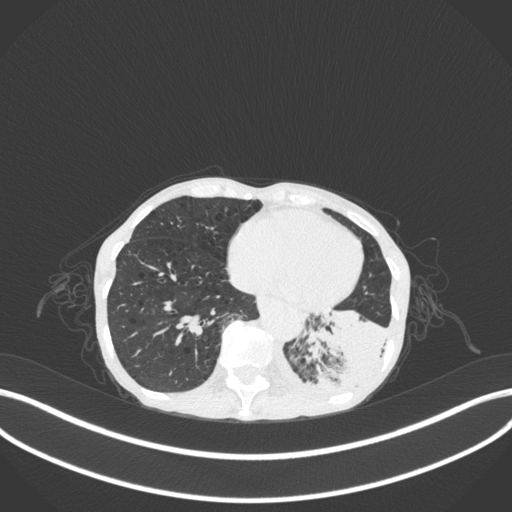
Chest CT, one axial slice; slice 64 of 347 in the series (ordered by position); reconstruction kernel B31f; 120 kVp; lung window (W 1500 / L -600 HU); 1 mm slice thickness; 512 × 512 image matrix, field of view 400 × 400 mm. Patient: female, 70 years. From the clinical record (not read from this slice): clinical TNM (as recorded): T3 N0 M0.
Outlined on this slice (bounding box drawn by a radiologist):
- lung tumour (recorded histology: small cell carcinoma): bounding box [x1, y1, x2, y2] px = [301, 298, 387, 407]